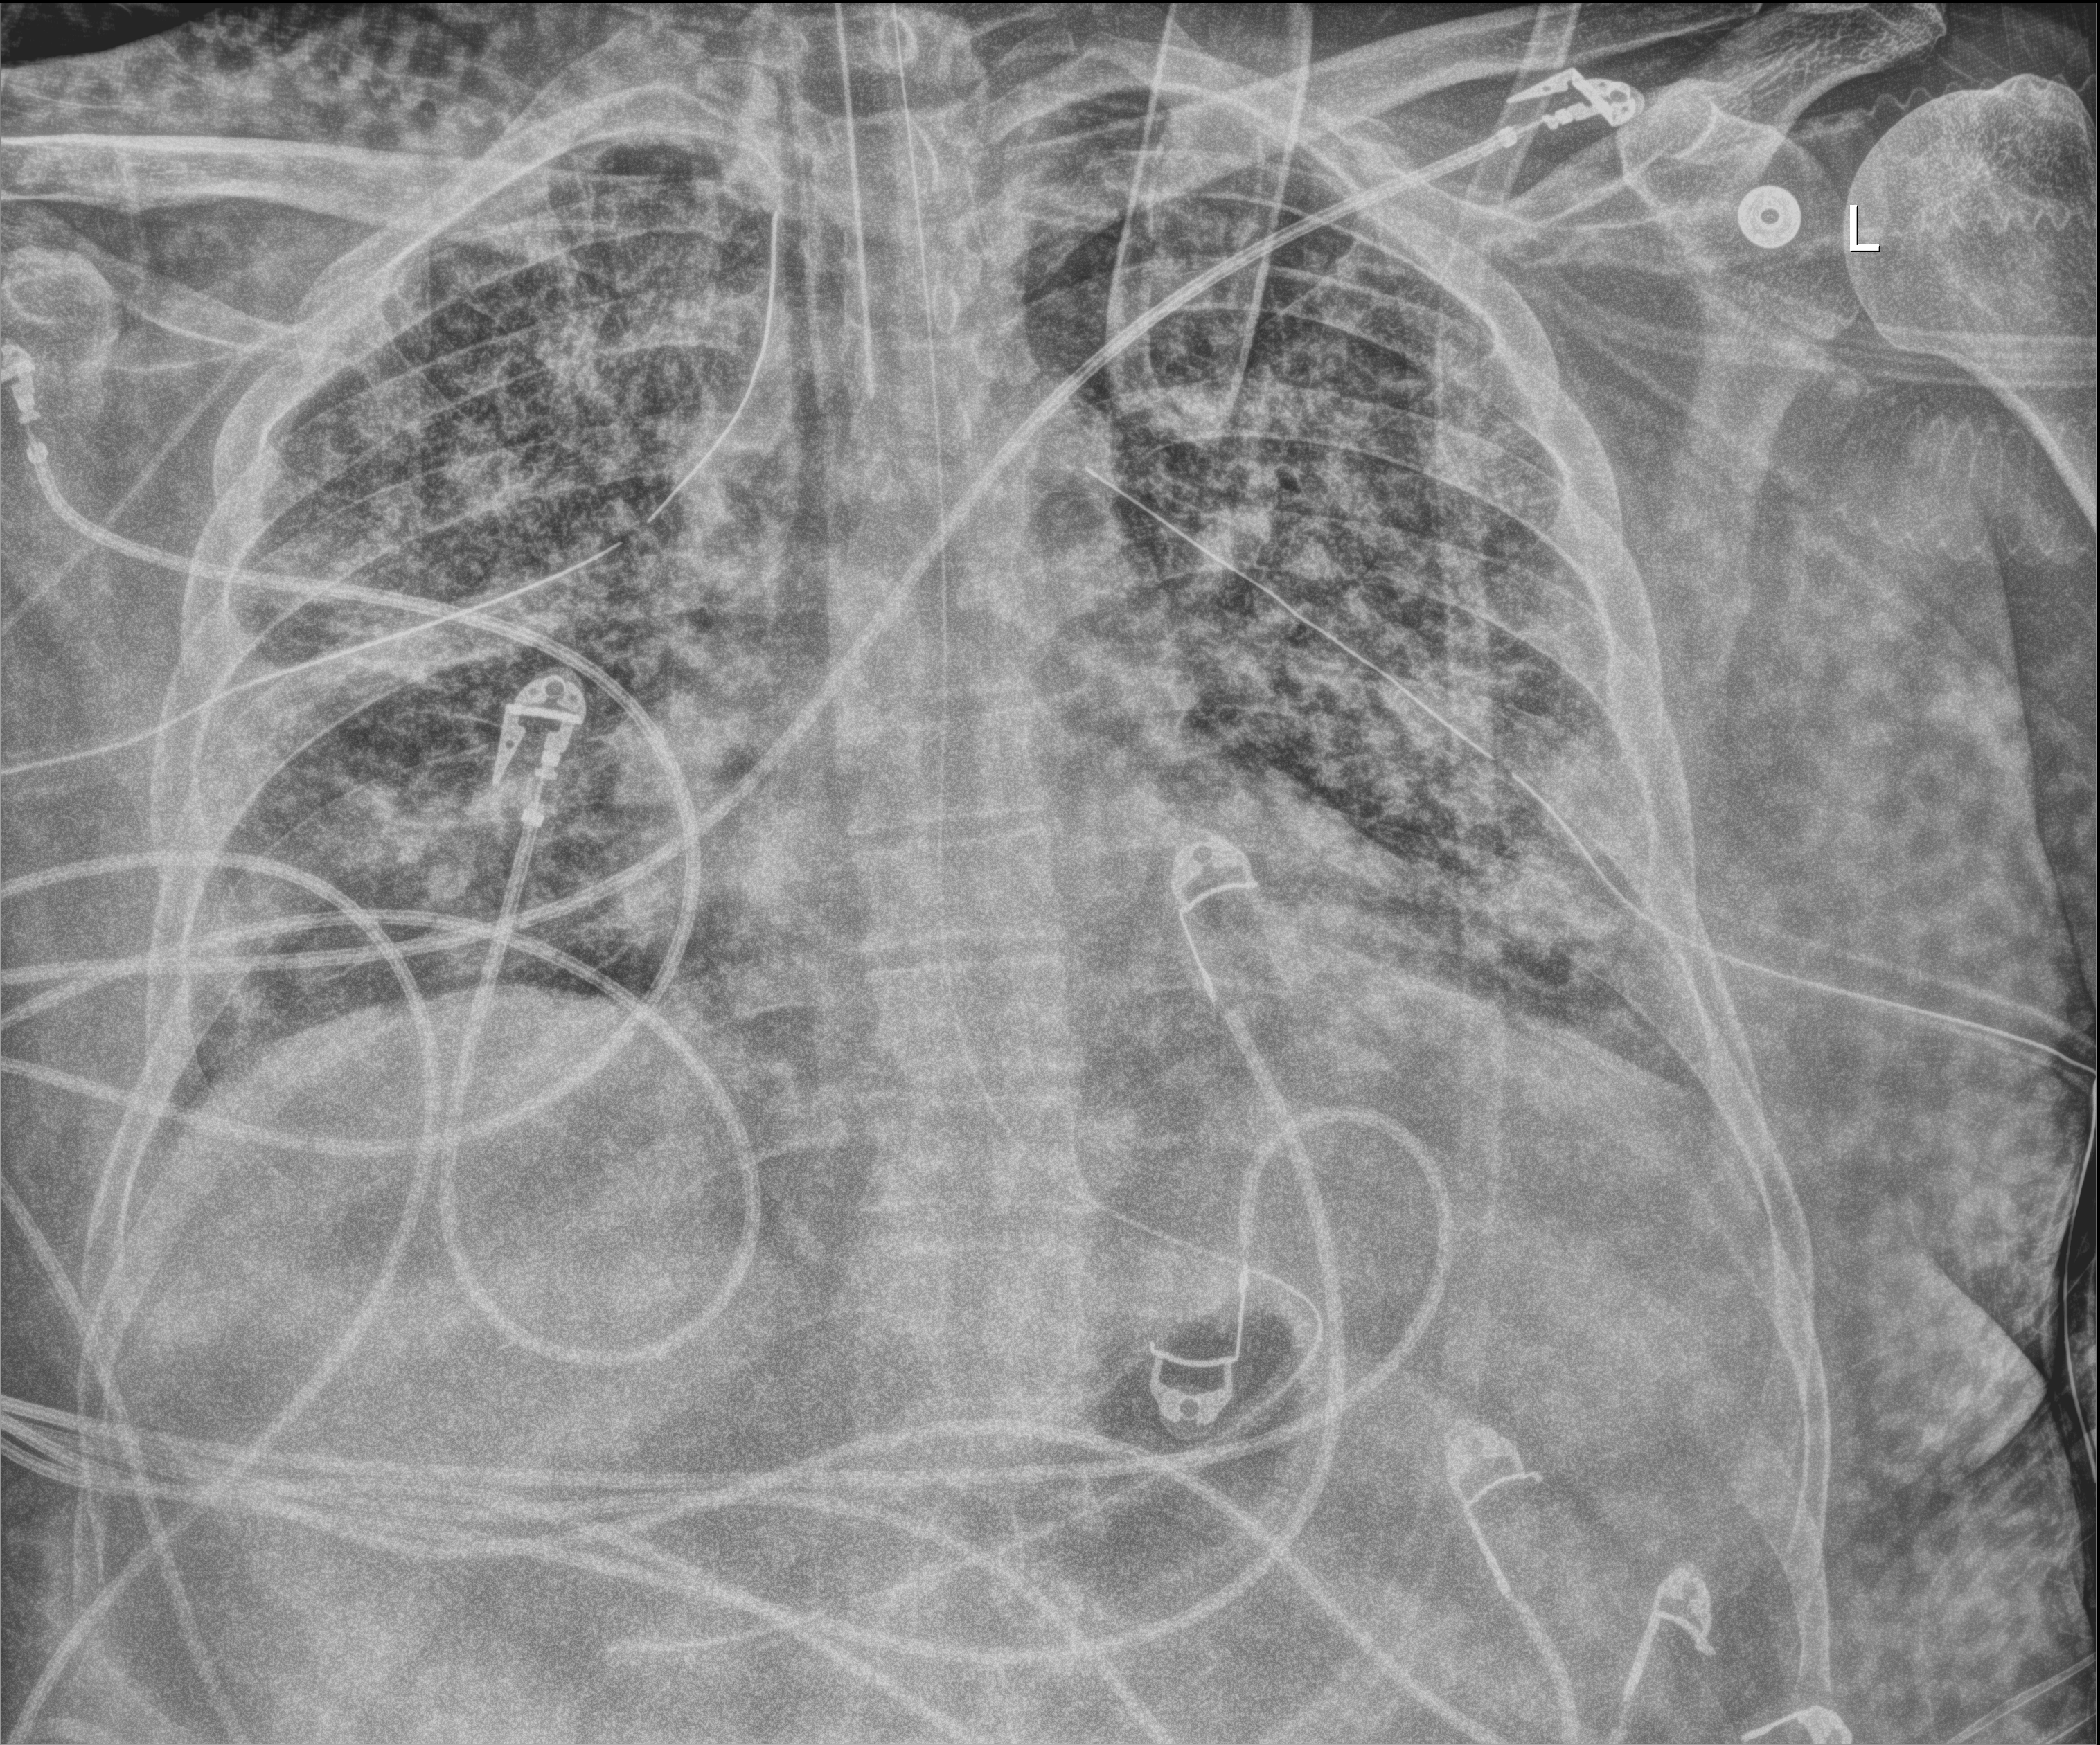
Chest X-ray, anteroposterior (AP) projection. Patient hospitalised with COVID-19; male, aged 18–59 years.
Hospital-stay facts (about this admission, not read from this image; timing relative to this image not recorded): smoking status (admission record): never.